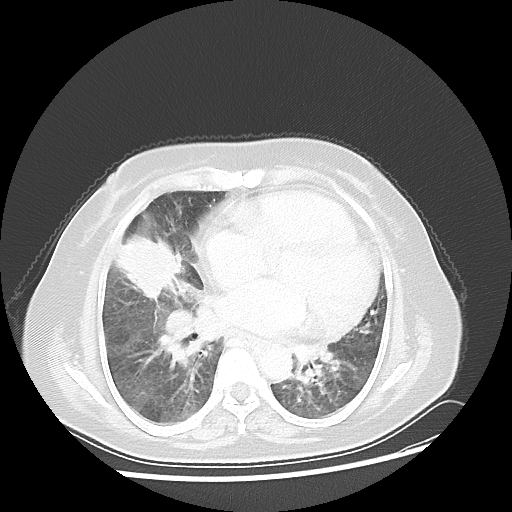
Chest CT, one axial slice; slice 20 of 45 in the series (ordered by position); reconstruction kernel LUNG; lung window (W 1500 / L -600 HU); 5 mm slice thickness; 512 × 512 image matrix, field of view 359 × 359 mm. Female patient, age 67 years. Case-level facts recorded for this patient, not image findings: clinical TNM (as recorded): T2a N3 M1a.
Structures marked on this image (bounding box drawn by a radiologist):
- lung tumour (recorded histology: adenocarcinoma): bounding box <119,233,181,300> (left, top, right, bottom; pixels)